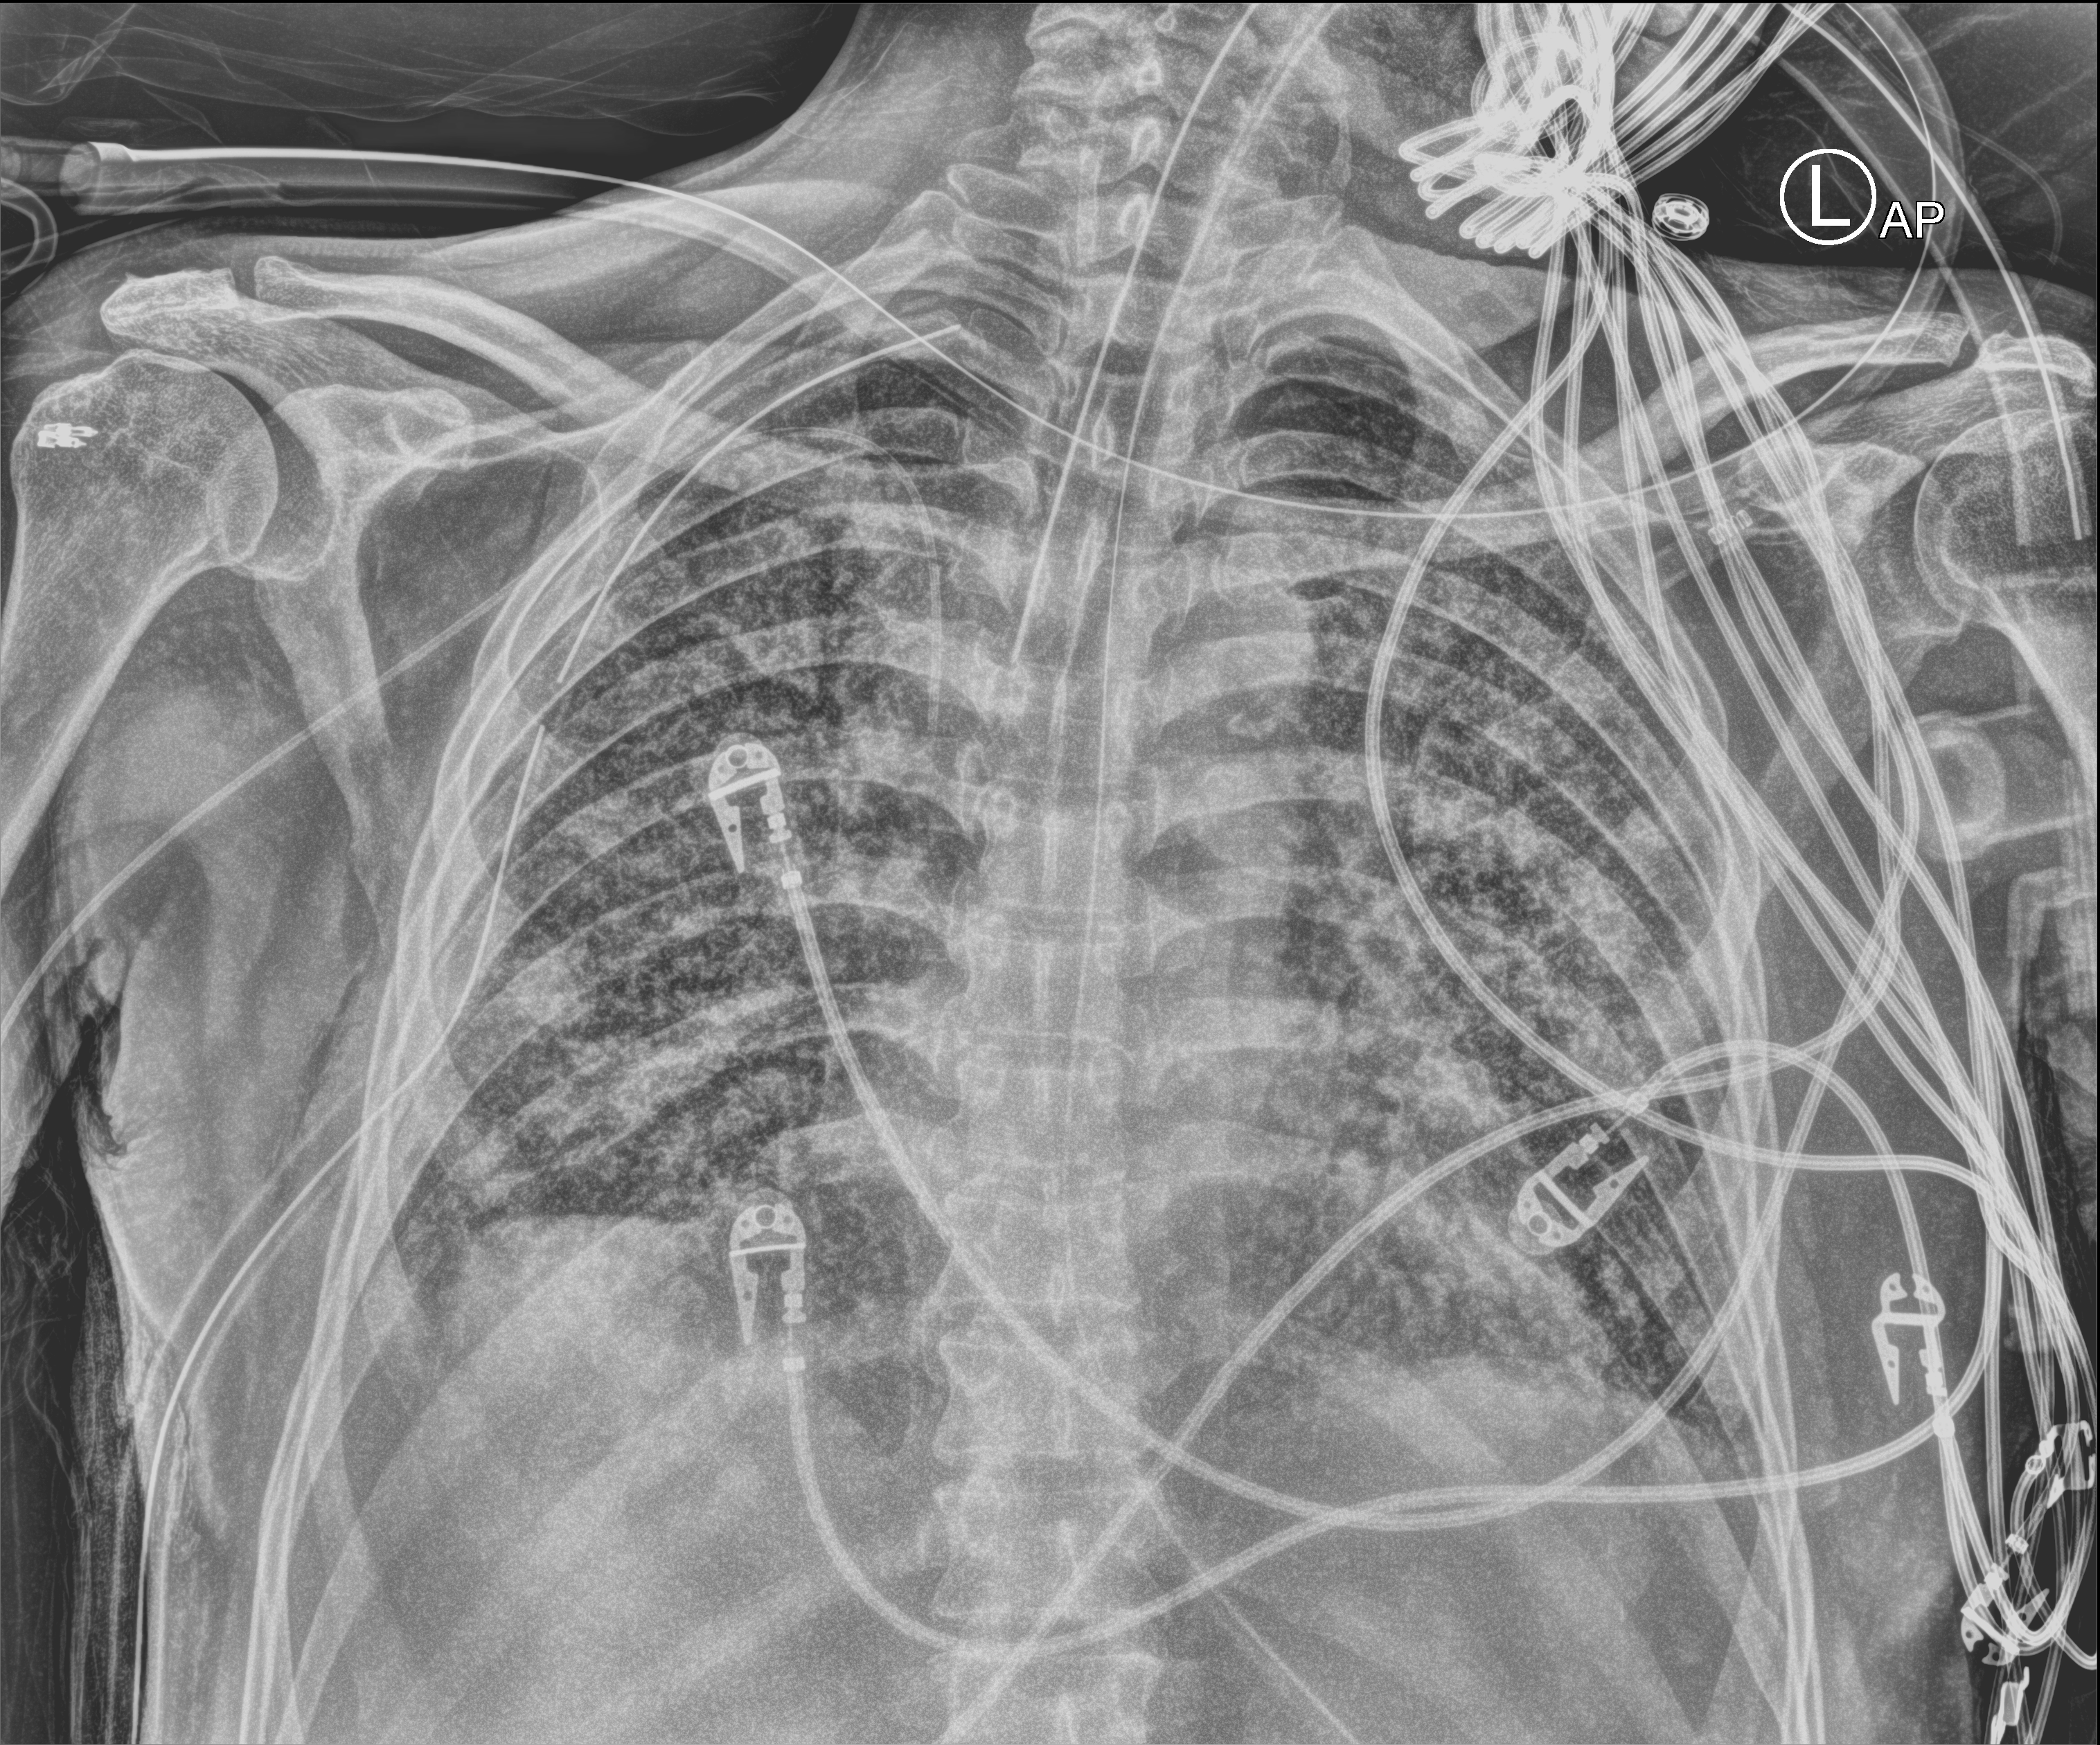
Portable chest radiograph, anteroposterior (AP) projection. Patient hospitalised with COVID-19; male, aged 60–74 years.
From the hospital-stay record, not from the radiograph (when in the stay this image was taken is not recorded): admitted to intensive care during this hospital stay: yes; mechanically ventilated during this hospital stay: yes.